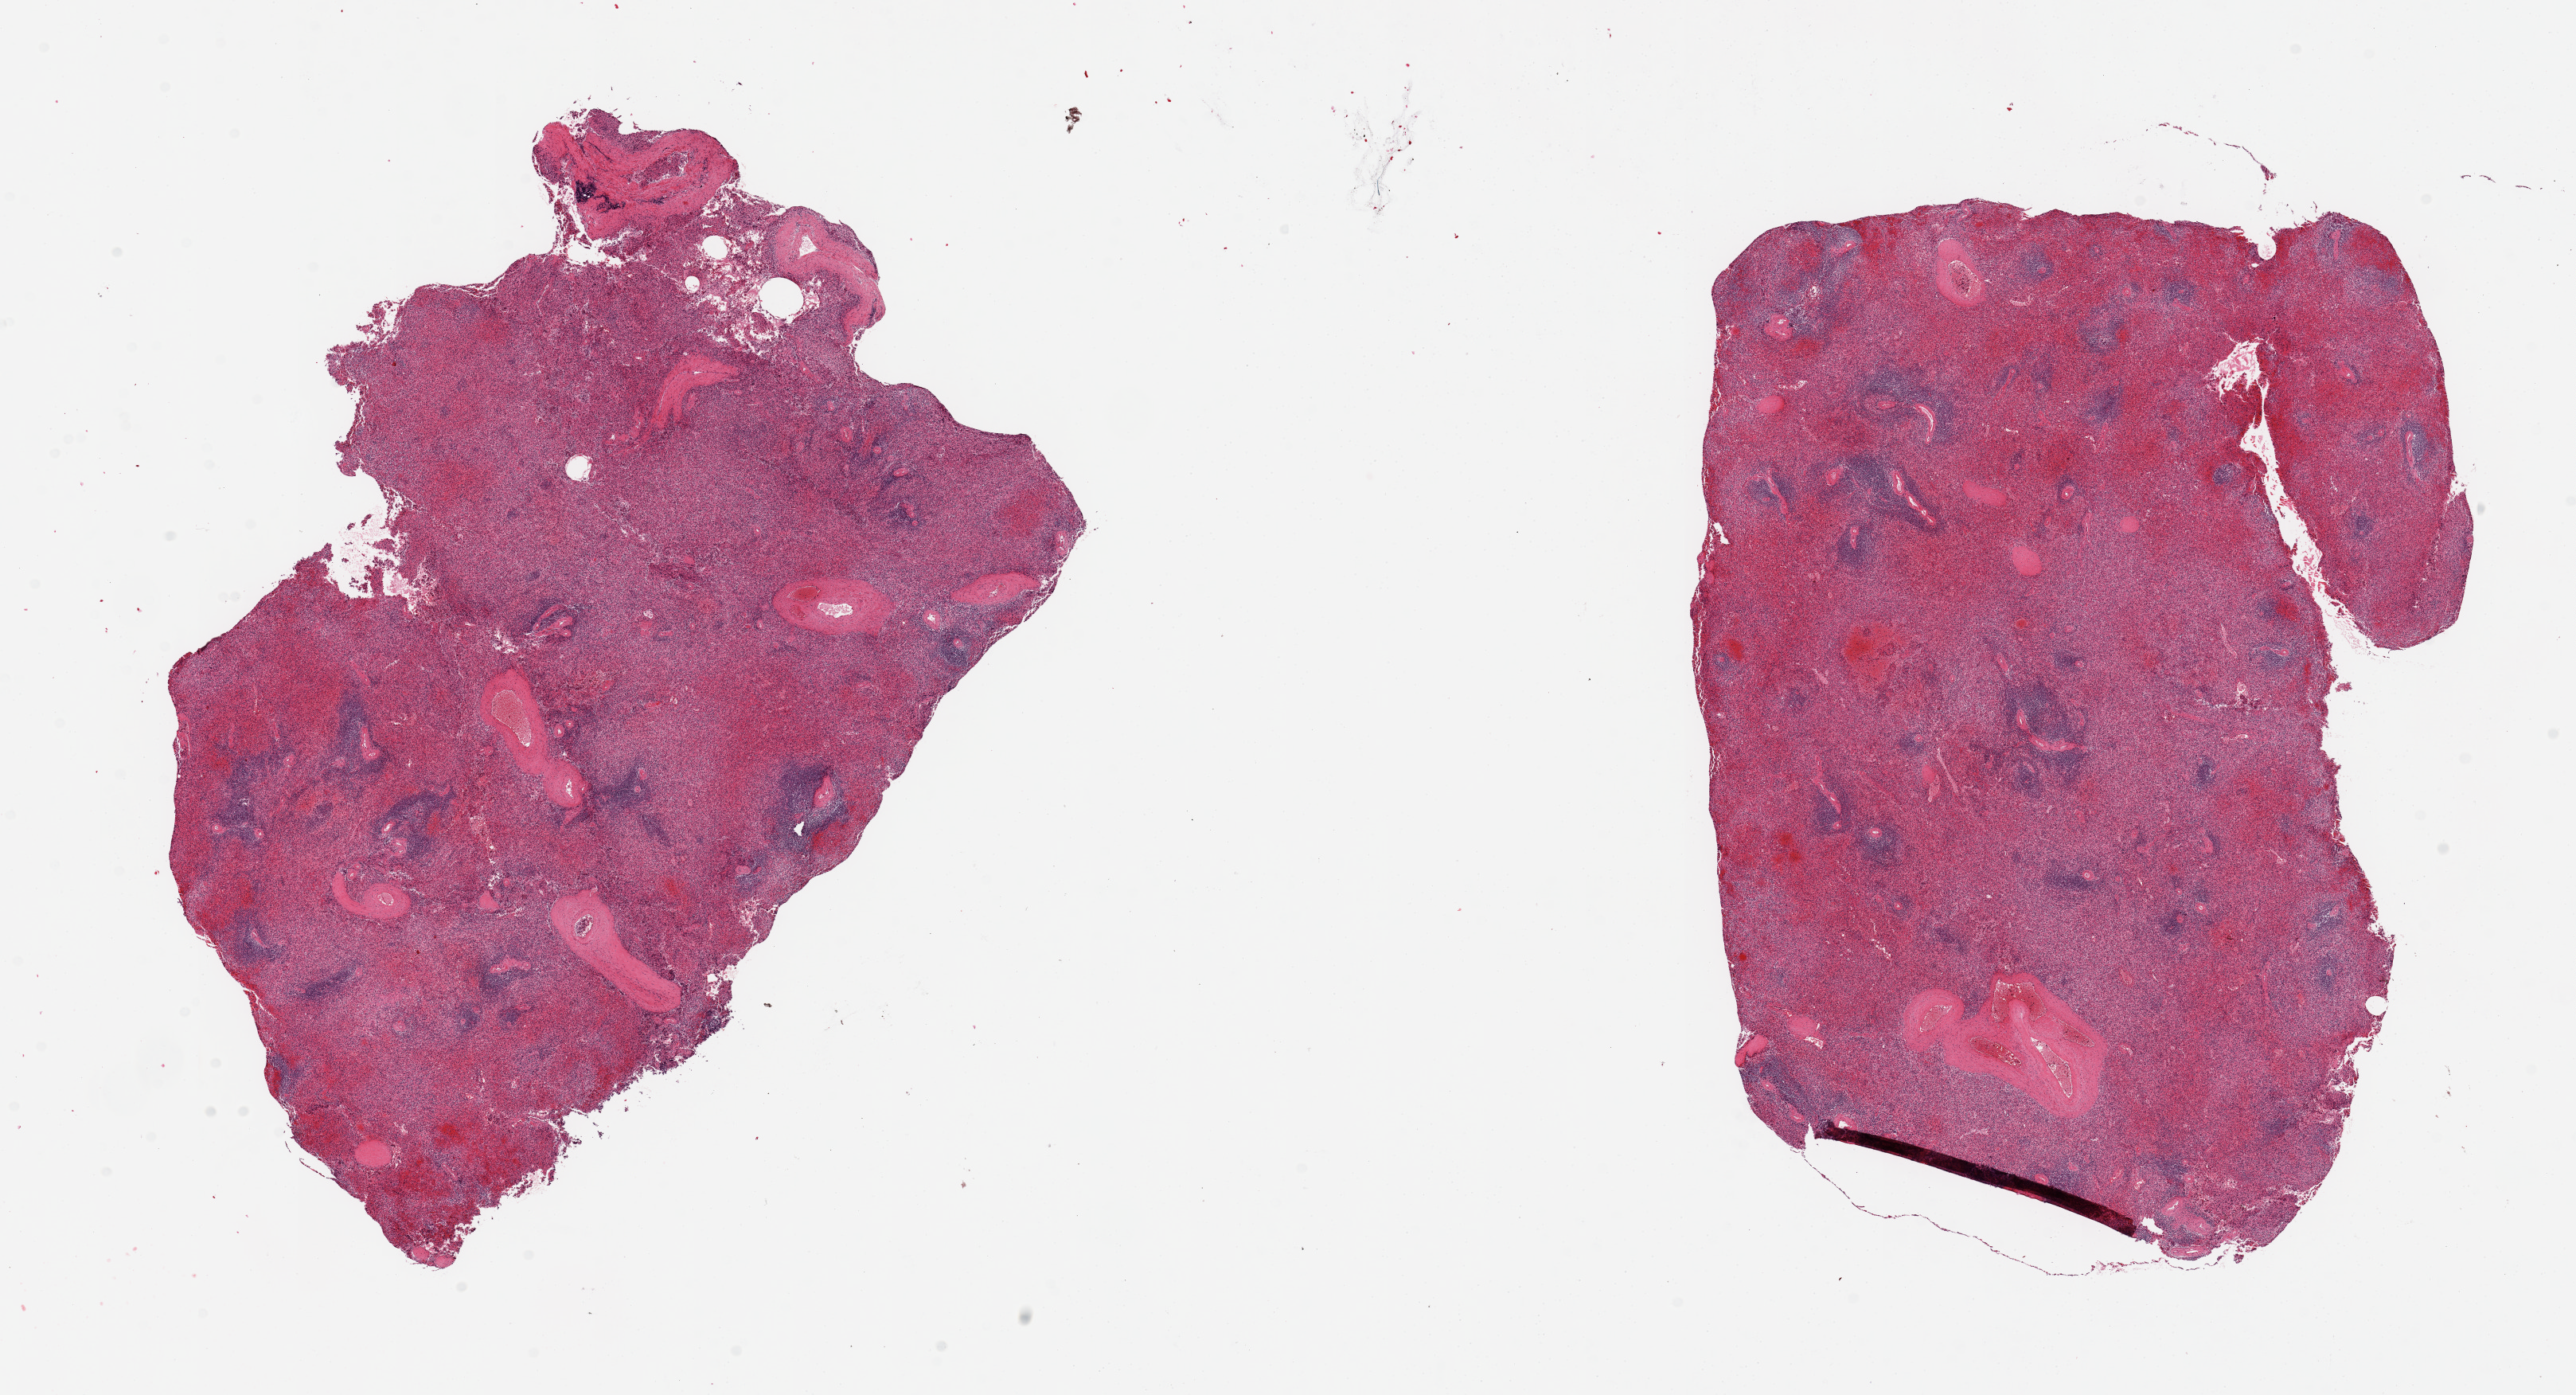
Digitized H&E-stained section, brightfield — whole scanned area (about 25.6 x 13.9 mm, from a 20x scan) shown as a low-resolution overview. PAXgene-fixed, paraffin-embedded tissue. Target tissue: spleen. Donor tissue sample. Donor sex: male.
Reviewer comment on this tissue sample: 2 pieces.